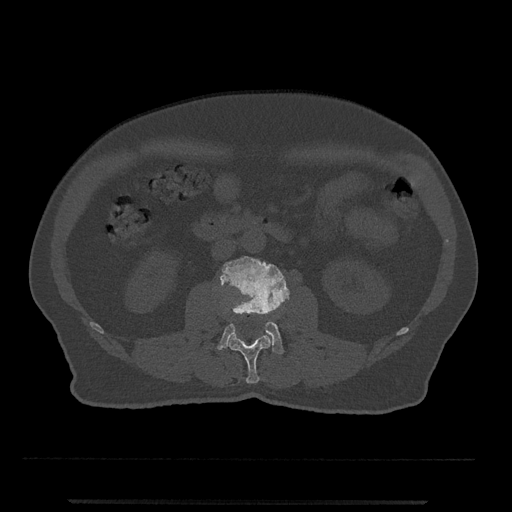
CT including the spine, one axial slice; slice 236 of 797 in the series (ordered by position); reconstruction kernel Br40s/3; 120 kVp; bone window (W 1800 / L 400 HU); 0.5 mm slice thickness; 512 × 512 image matrix, field of view 419 × 419 mm. Male patient, age 63 years. Case-level facts recorded for this patient, not image findings: primary cancer: prostate.
Structures marked on this image (semi-automatically segmented with operator editing):
- L2 vertebra: bounding box [x1, y1, x2, y2] px = [228, 332, 271, 383]
- L3 vertebra: [217, 256, 290, 354]